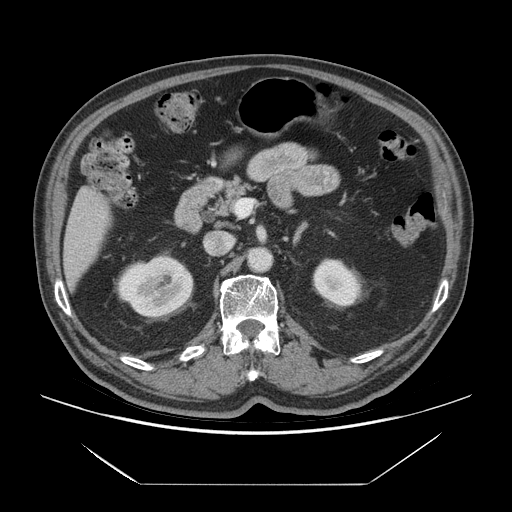
Contrast-enhanced abdominal CT (liver protocol), one axial slice; position 27 of 75 along the scan axis; reconstruction kernel STANDARD; 140 kVp; soft-tissue window (W 400 / L 40 HU); 2.5 mm slice thickness; 512 × 512 image matrix. Case-level facts recorded for this patient, not image findings: diagnosis: hepatocellular carcinoma (patient treated with transarterial chemoembolisation; whether this scan precedes or follows treatment is not stated here); TNM stage (as recorded): Stage-I; Child-Pugh class: A; tumour differentiation: well differentiated; tumour nodularity: uninodular.
Annotated regions visible in this slice (semi-automatic segmentation, software-assisted and operator-edited):
- liver parenchyma outside the tumour (the mass and vessels are separate outlines, so this box may not span the whole liver): bounding box [x1, y1, x2, y2] px = [62, 186, 110, 289]